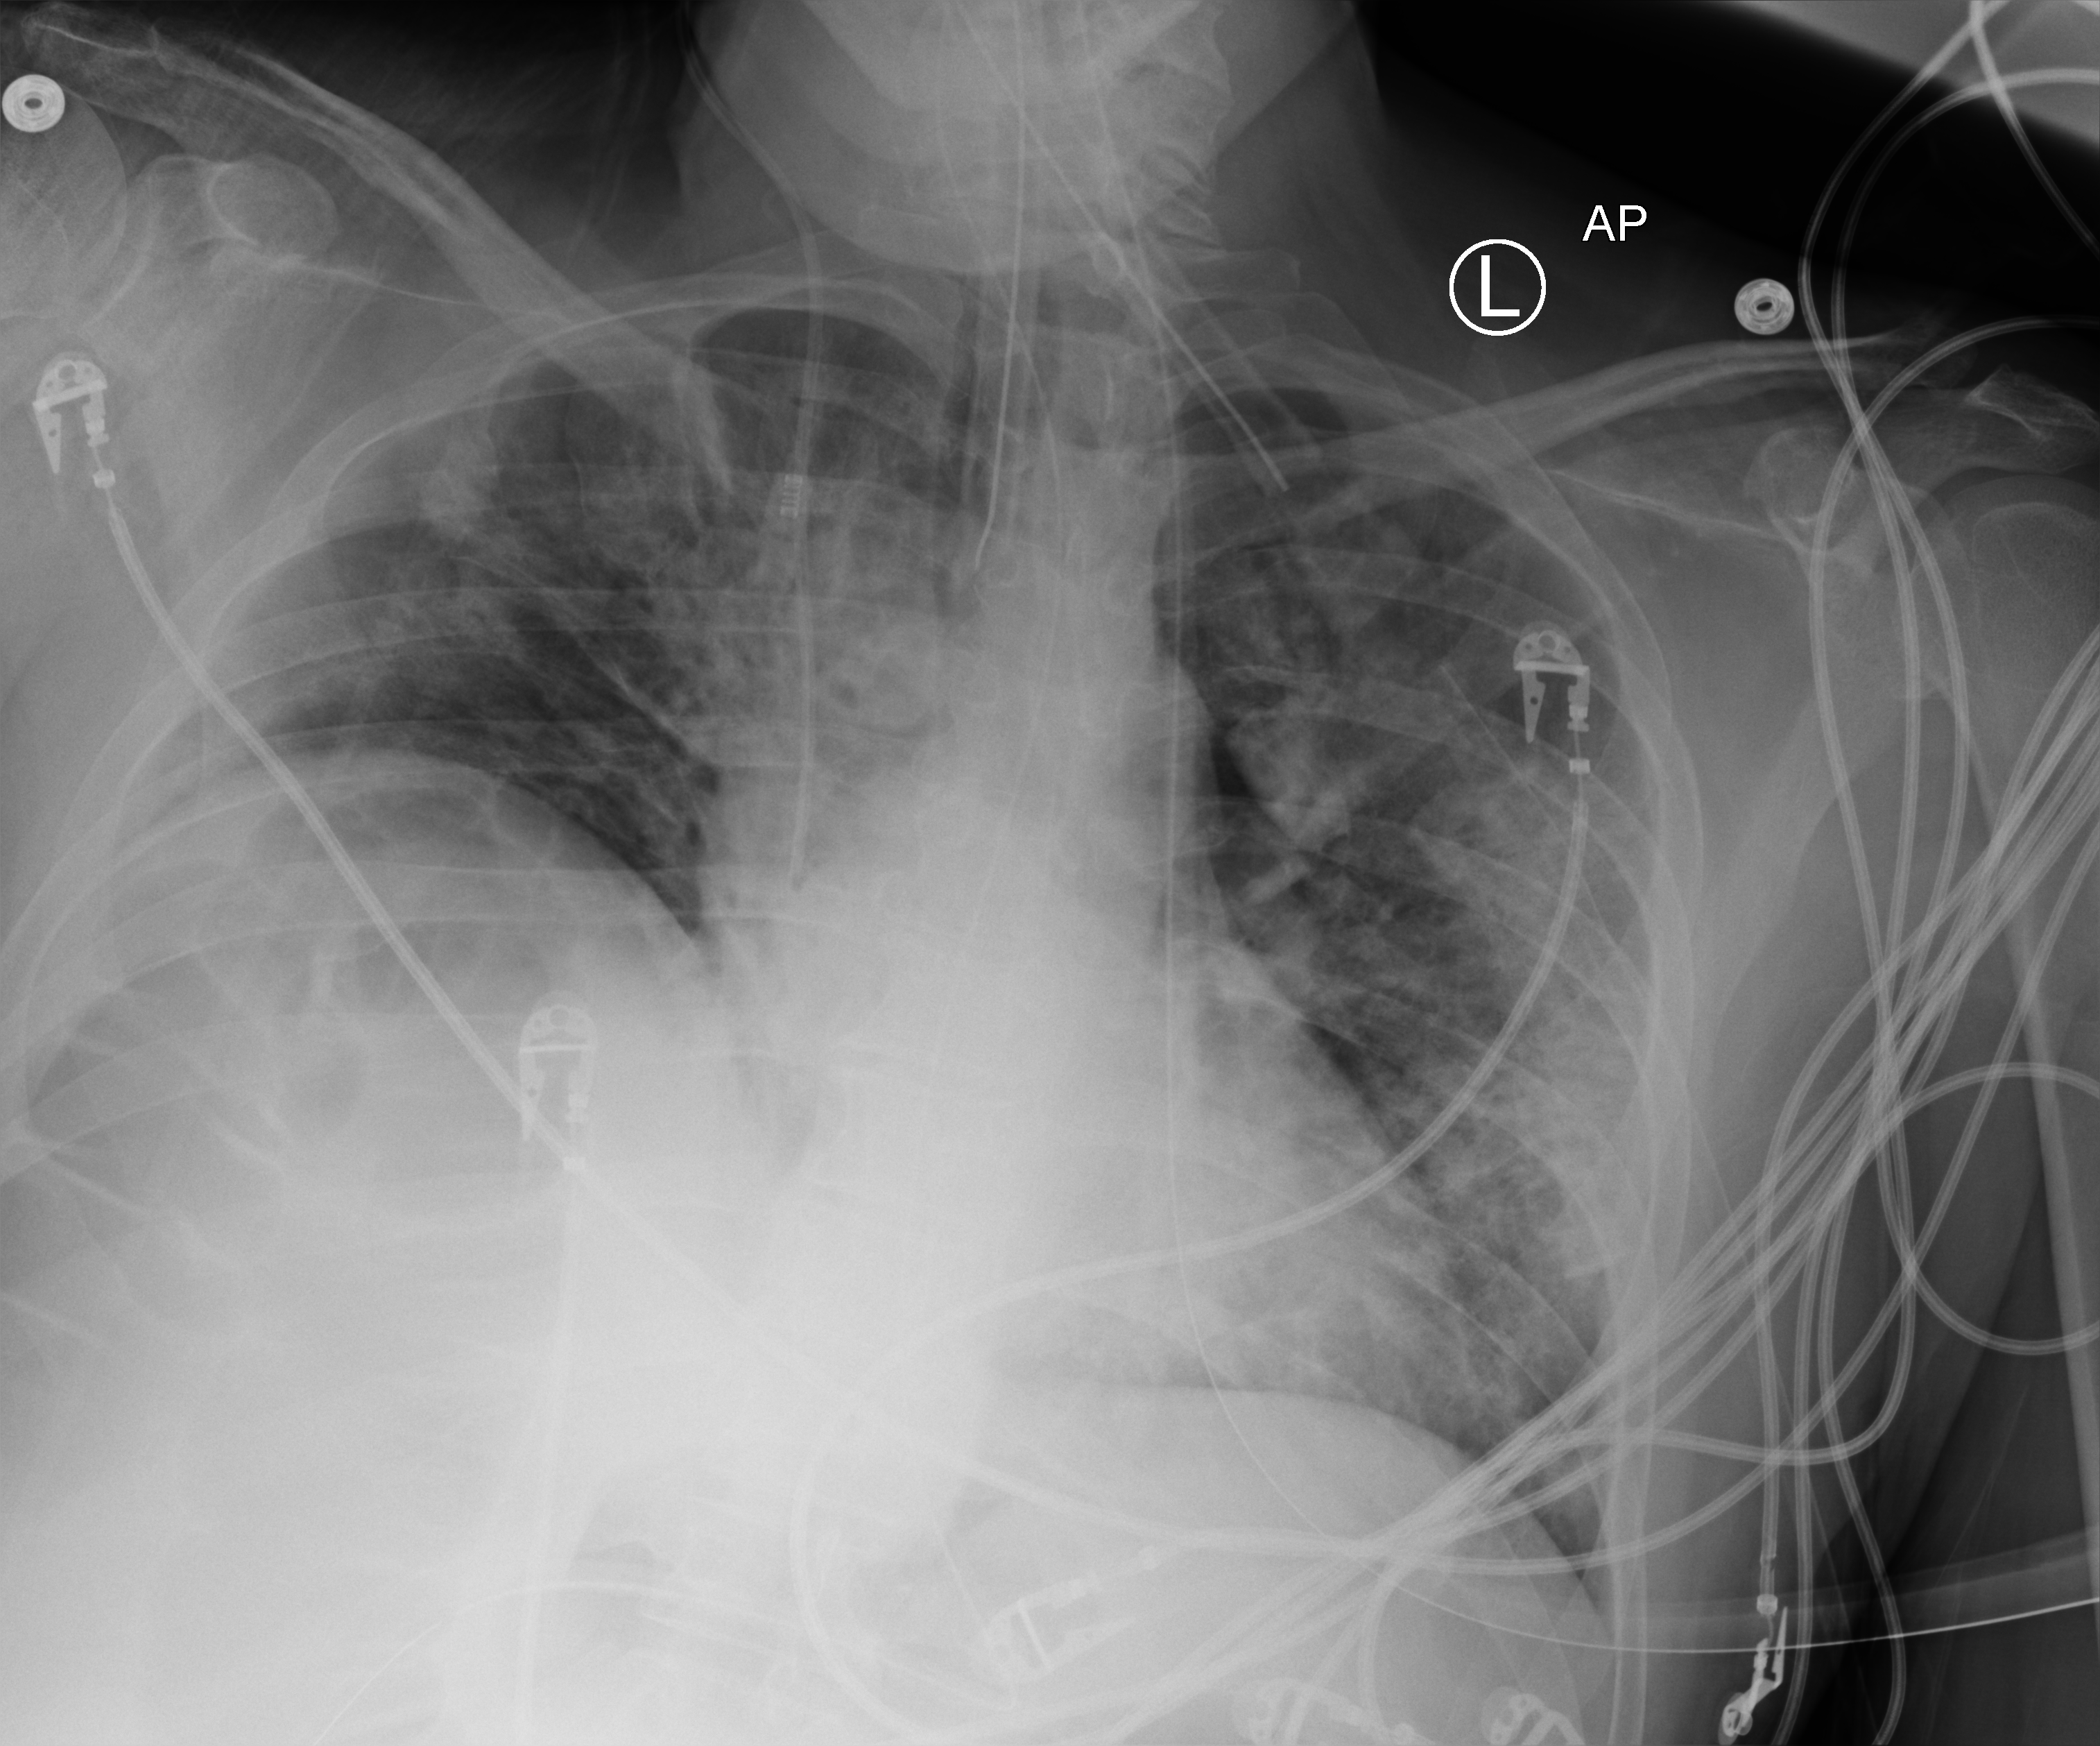
Portable chest radiograph; anteroposterior (AP) projection. Male patient hospitalised with COVID-19, age 18–59 years.
Admission-level facts for this patient (not findings on this image; timing relative to this image not recorded): mechanically ventilated during this hospital stay: yes; admitted to intensive care during this hospital stay: yes.